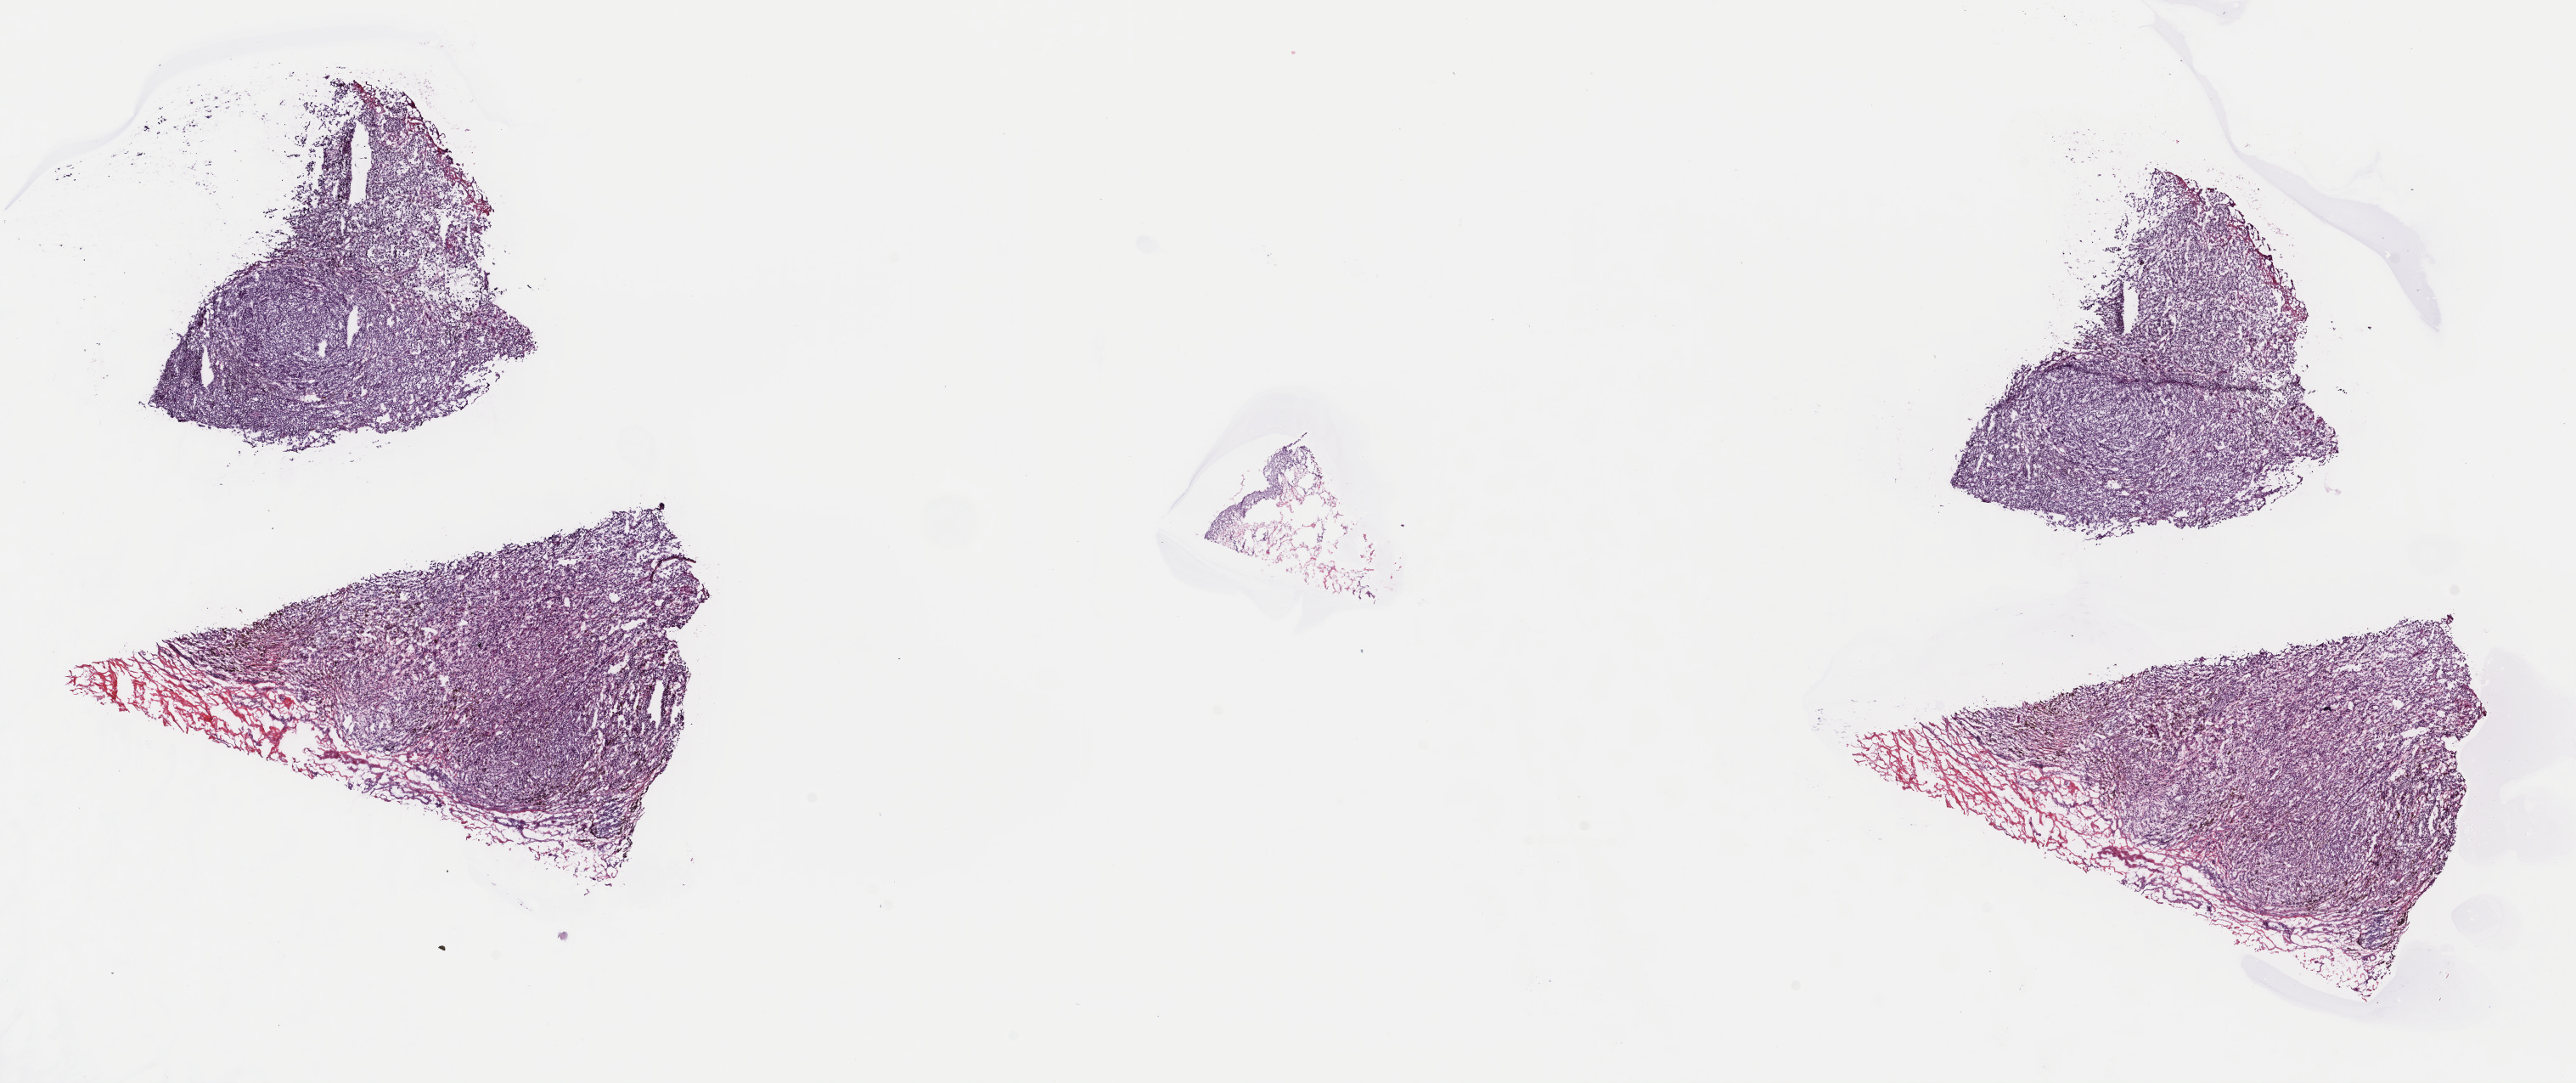
H&E-stained whole-slide image, low-resolution overview of the scanned area, about 23.9 x 10.1 mm (from a 40x scan). Frozen section from the top of the tissue portion. Sample: primary tumour, skin. Patient: female, age at initial diagnosis 76 years. Slide review estimates, as recorded: tumour cells 80%, tumour nuclei 80%, normal cells 0%, stromal cells 20%, necrosis 0%. Inflammatory infiltration, as recorded: lymphocyte infiltration 3%, monocyte infiltration 0%, neutrophil infiltration 0%.
AJCC pathologic stage: IIA (7th edition). TNM: T3a N0 M0. Diagnosis: Malignant melanoma, NOS.